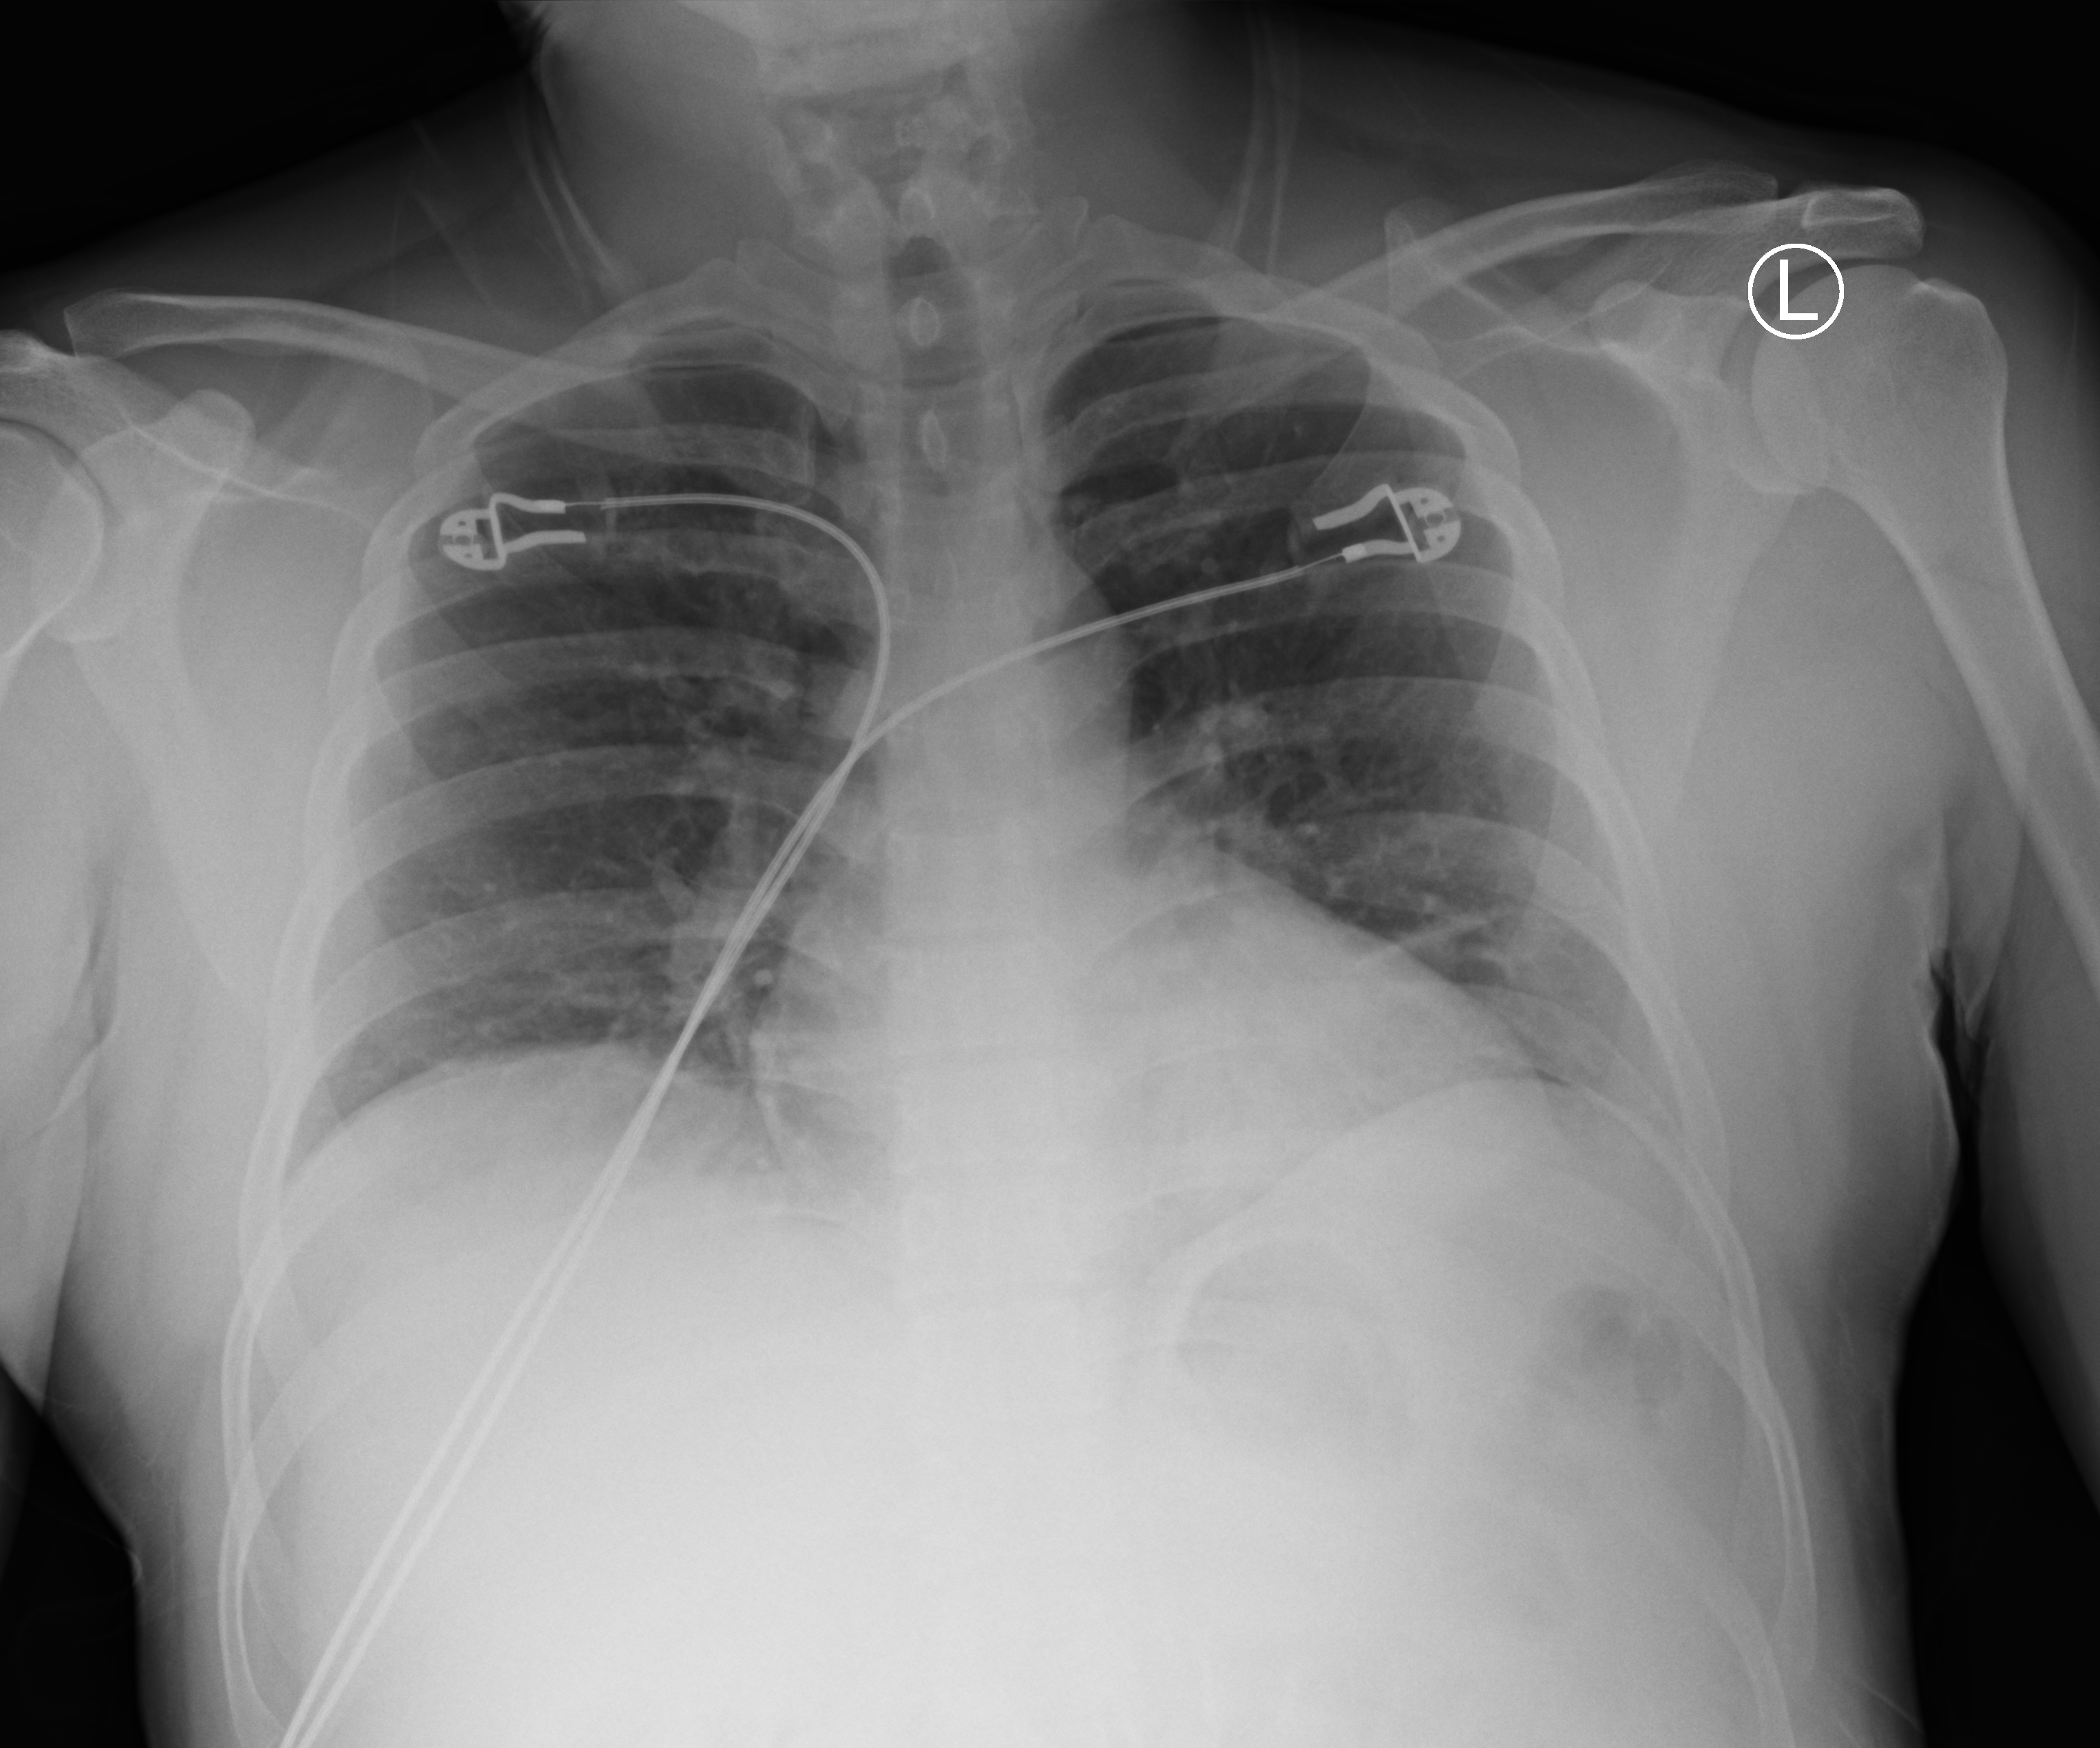
Bedside chest radiograph (computed radiography); anteroposterior (AP) projection. Male patient hospitalised with COVID-19, age 18–59 years.
Admission-level facts for this patient (not findings on this image; timing relative to this image not recorded):
- mechanically ventilated during this hospital stay: no
- chronic kidney disease (admission record): no
- hypertension (admission record): no